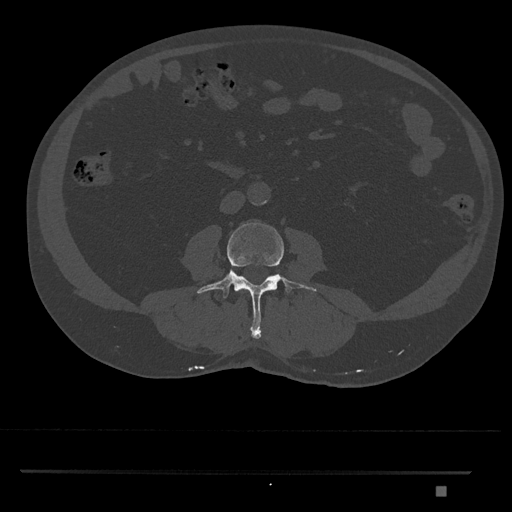
CT including the spine, one axial slice. Position 679 of 1134 along the scan axis. Reconstruction kernel Br40s/3. 120 kVp. Bone window (W 1800 / L 400 HU). 512 × 512 image matrix, field of view 429 × 429 mm. Patient: male, 65 years. From the clinical record (not read from this slice): primary cancer: prostate.
Structures marked on this image (semi-automatically segmented with operator editing):
- L3 vertebra: bounding box <197,222,317,339> (left, top, right, bottom; pixels)